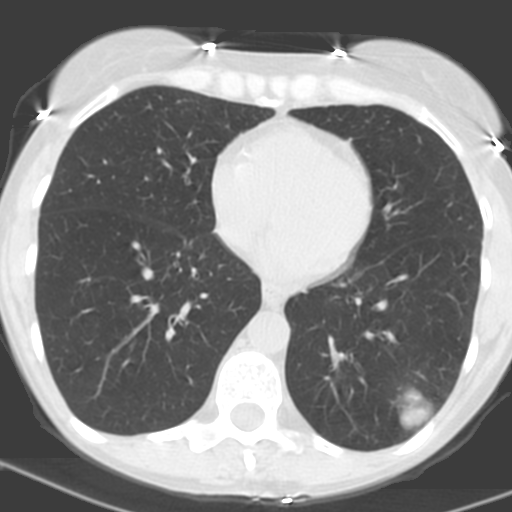
Low-dose screening chest CT, one axial slice; position 61 of 156 along the scan axis; 120 kVp; lung window (W 1500 / L -600 HU); 3.2 mm slice thickness; 512 × 512 image matrix, field of view 262 × 262 mm.
Outlined on this slice (manually delineated by an expert):
- lesion 1 (tumor, lower lobe of left lung): bounding box [x1, y1, x2, y2] px = [400, 389, 432, 429]